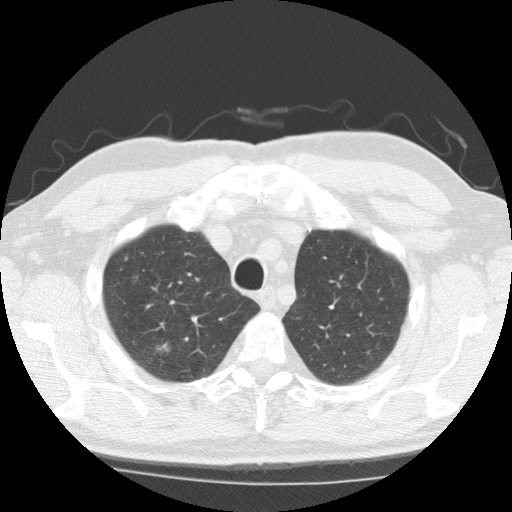
Low-dose screening chest CT, one axial slice; slice 158 of 196 in the series (ordered by position); 120 kVp; lung window (W 1500 / L -600 HU); 2.5 mm slice thickness; 512 × 512 image matrix, field of view 350 × 350 mm.
Structures marked on this image (manually delineated by an expert):
- lesion 1 (tumor, upper lobe of right lung): bounding box [x1, y1, x2, y2] px = [152, 342, 173, 357]